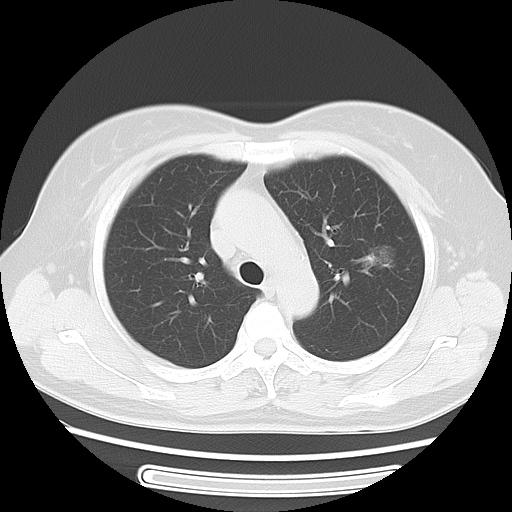
Chest CT, one axial slice. Slice 35 of 52 in the series (ordered by position). Reconstruction kernel LUNG. 120 kVp. Lung window (W 1500 / L -600 HU). 512 × 512 image matrix, field of view 350 × 350 mm. Patient: female, 54 years. Case-level facts recorded for this patient, not image findings: clinical TNM (as recorded): T1c N0 M0.
Structures marked on this image (bounding box drawn by a radiologist):
- lung tumour (recorded histology: adenocarcinoma): bounding box <351,240,411,282> (left, top, right, bottom; pixels)